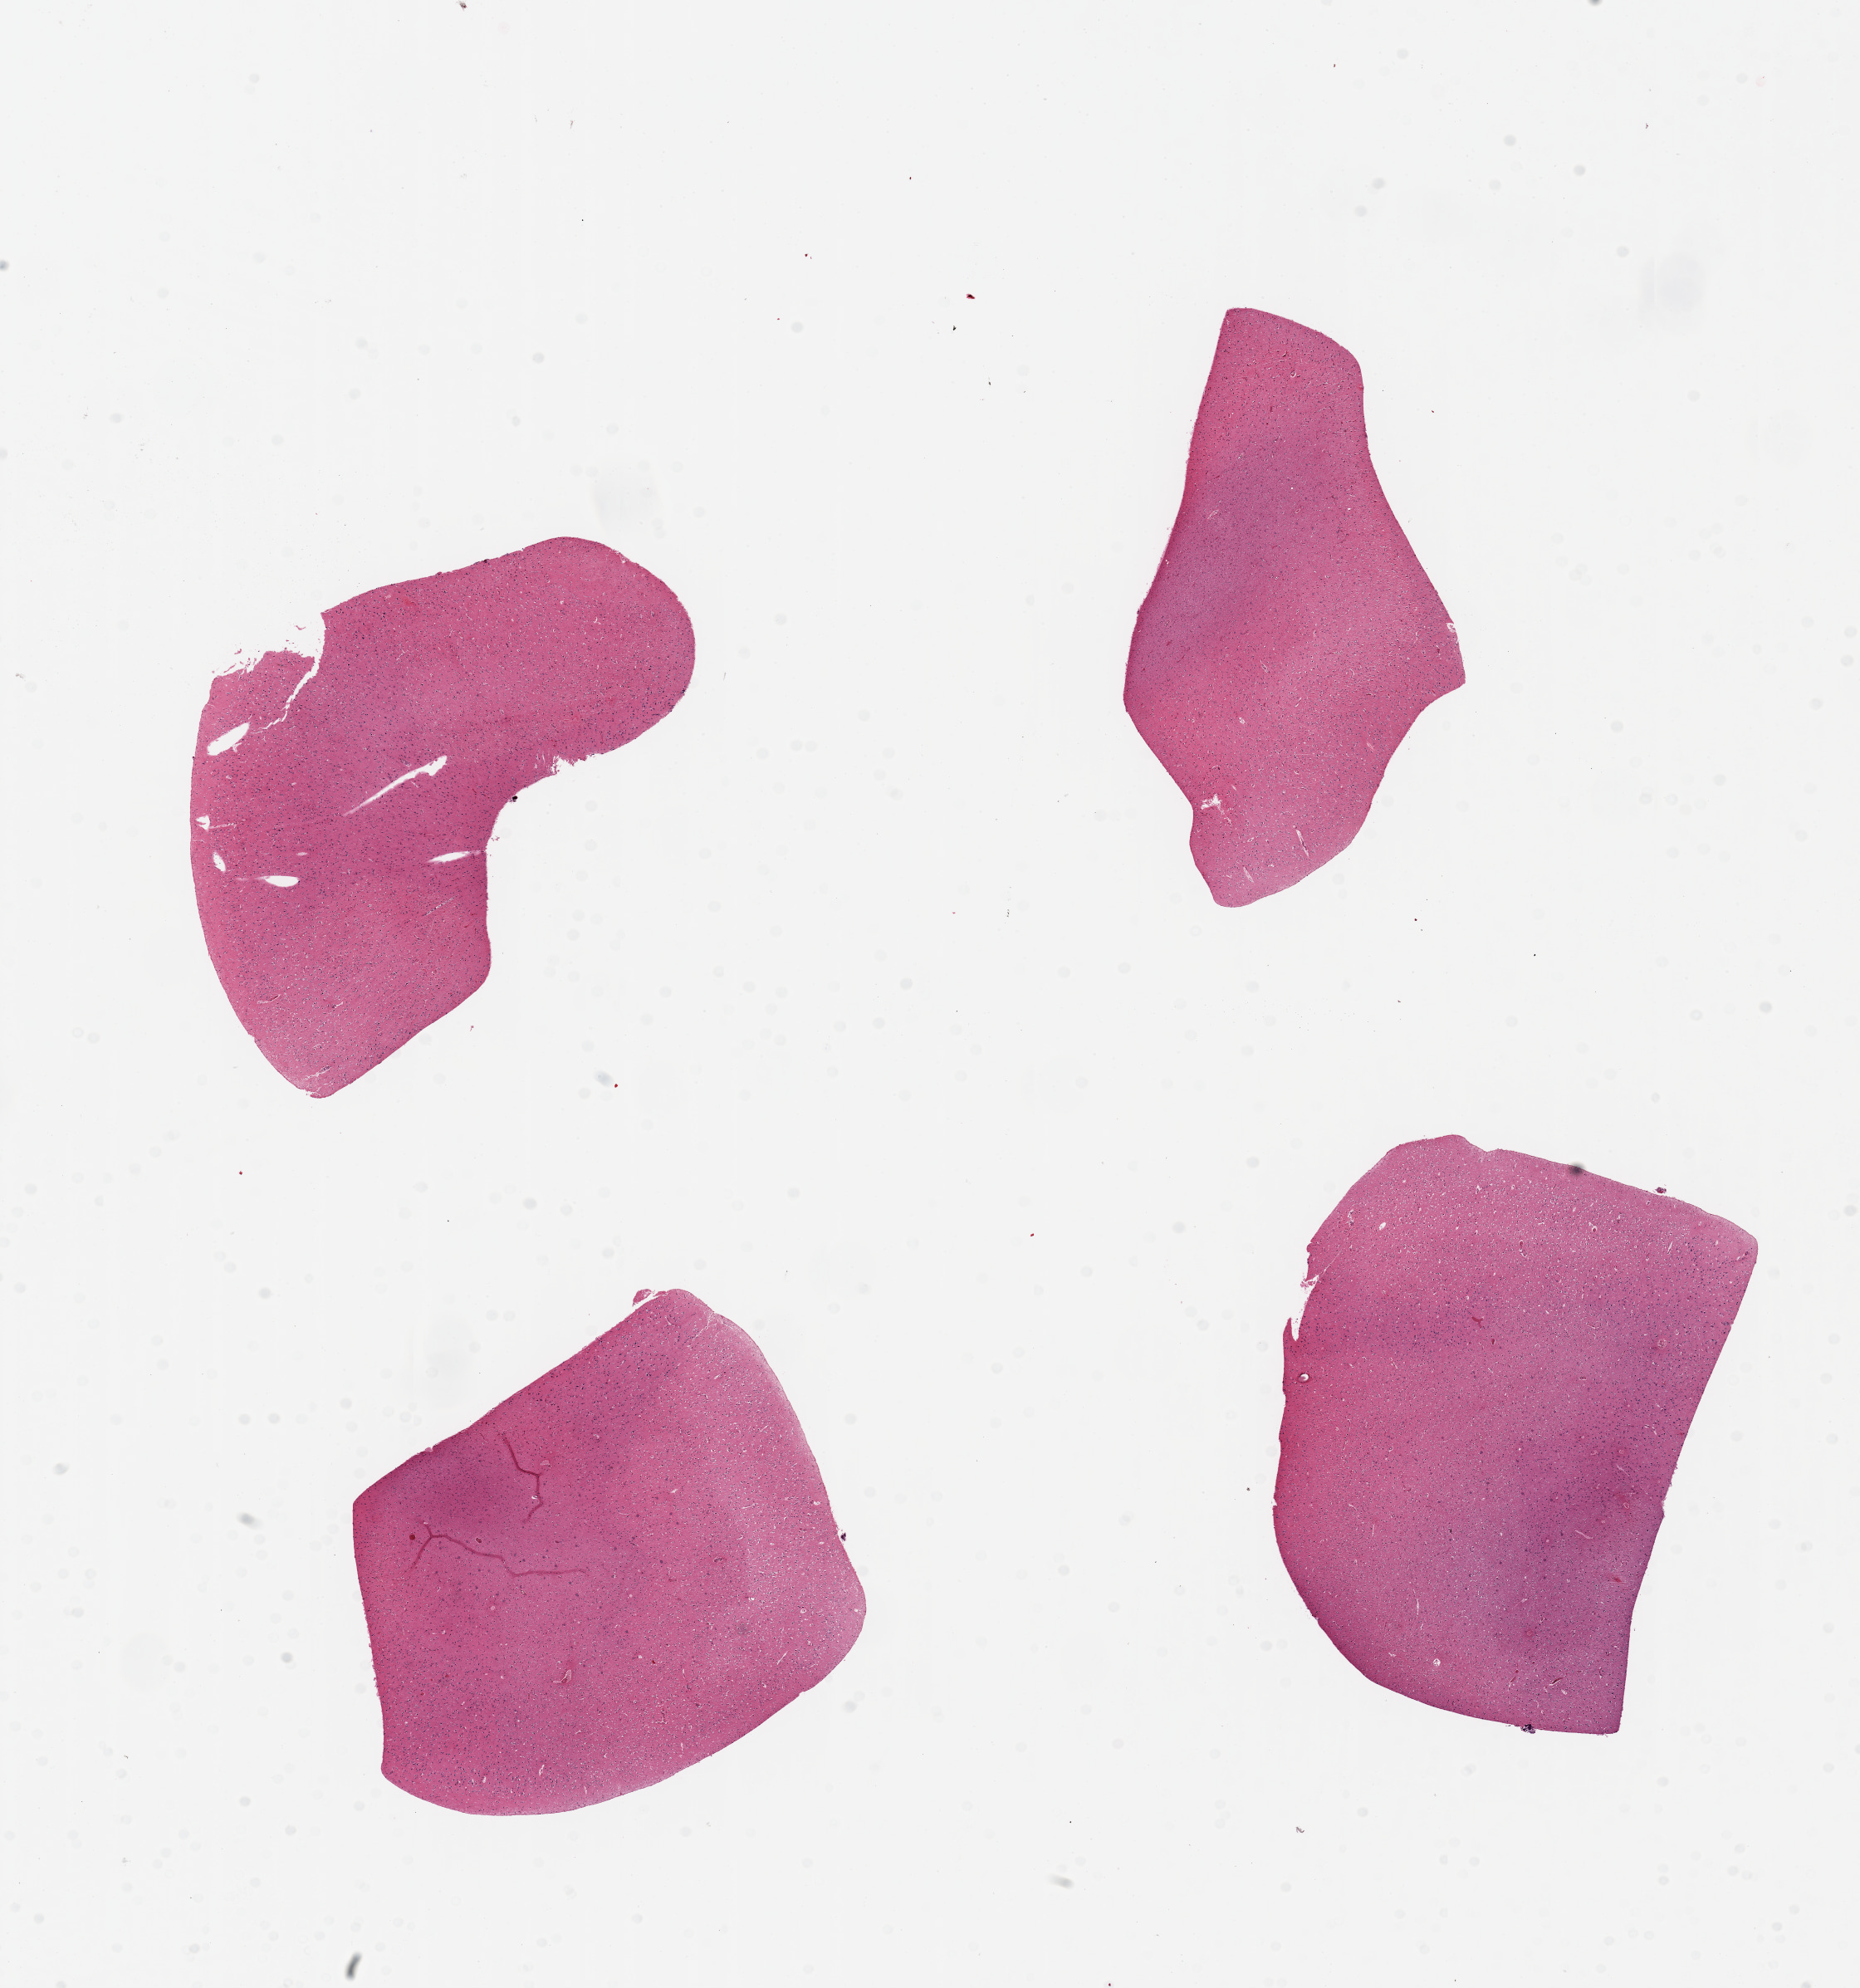
Digitized hematoxylin and eosin (H&E)-stained section, low-resolution overview of the scanned area, about 17.7 x 18.9 mm, PAXgene-fixed, paraffin-embedded tissue, section of cerebral cortex (target tissue), donor tissue sample. Donor sex: male.
• reviewer comment on this tissue sample: 4 pieces ~5x4 mm